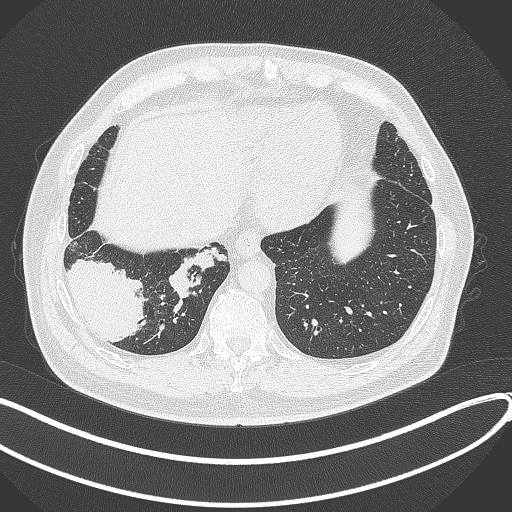
Chest CT, one axial slice. Position 78 of 360 along the scan axis. Lung window (W 1500 / L -600 HU). 1 mm slice thickness. 512 × 512 image matrix. Patient: male, 59 years.
Structures marked on this image (rectangle marked by the reading radiologist):
- lung tumour (recorded histology: adenocarcinoma): bounding box [x1, y1, x2, y2] px = [65, 256, 148, 344]